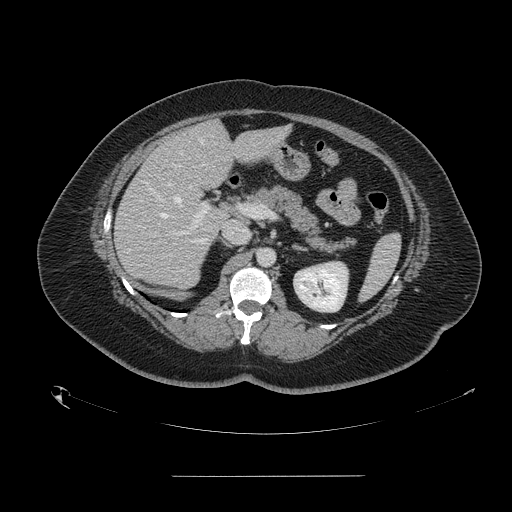
Contrast-enhanced abdominal CT, one axial slice. Slice 84 of 164 in the series (ordered by position). Soft-tissue window (W 400 / L 40 HU). 2.5 mm slice thickness. 512 × 512 image matrix, field of view 495 × 495 mm. Female patient, age 52 years. From the clinical record (not read from this slice): diagnosis: colorectal cancer liver metastases, imaged before liver resection; multiple liver metastases: yes; largest metastasis: 3.5 cm; chemotherapy before resection: no.
Outlined on this slice (outlined manually by an expert reader):
- hepatic veins: bounding box [x1, y1, x2, y2] px = [149, 139, 202, 218]
- liver: [114, 121, 286, 288]
- planned liver remnant (the part of the liver to remain after resection): [177, 120, 286, 189]
- portal vein (with intrahepatic branches): [168, 183, 207, 235]